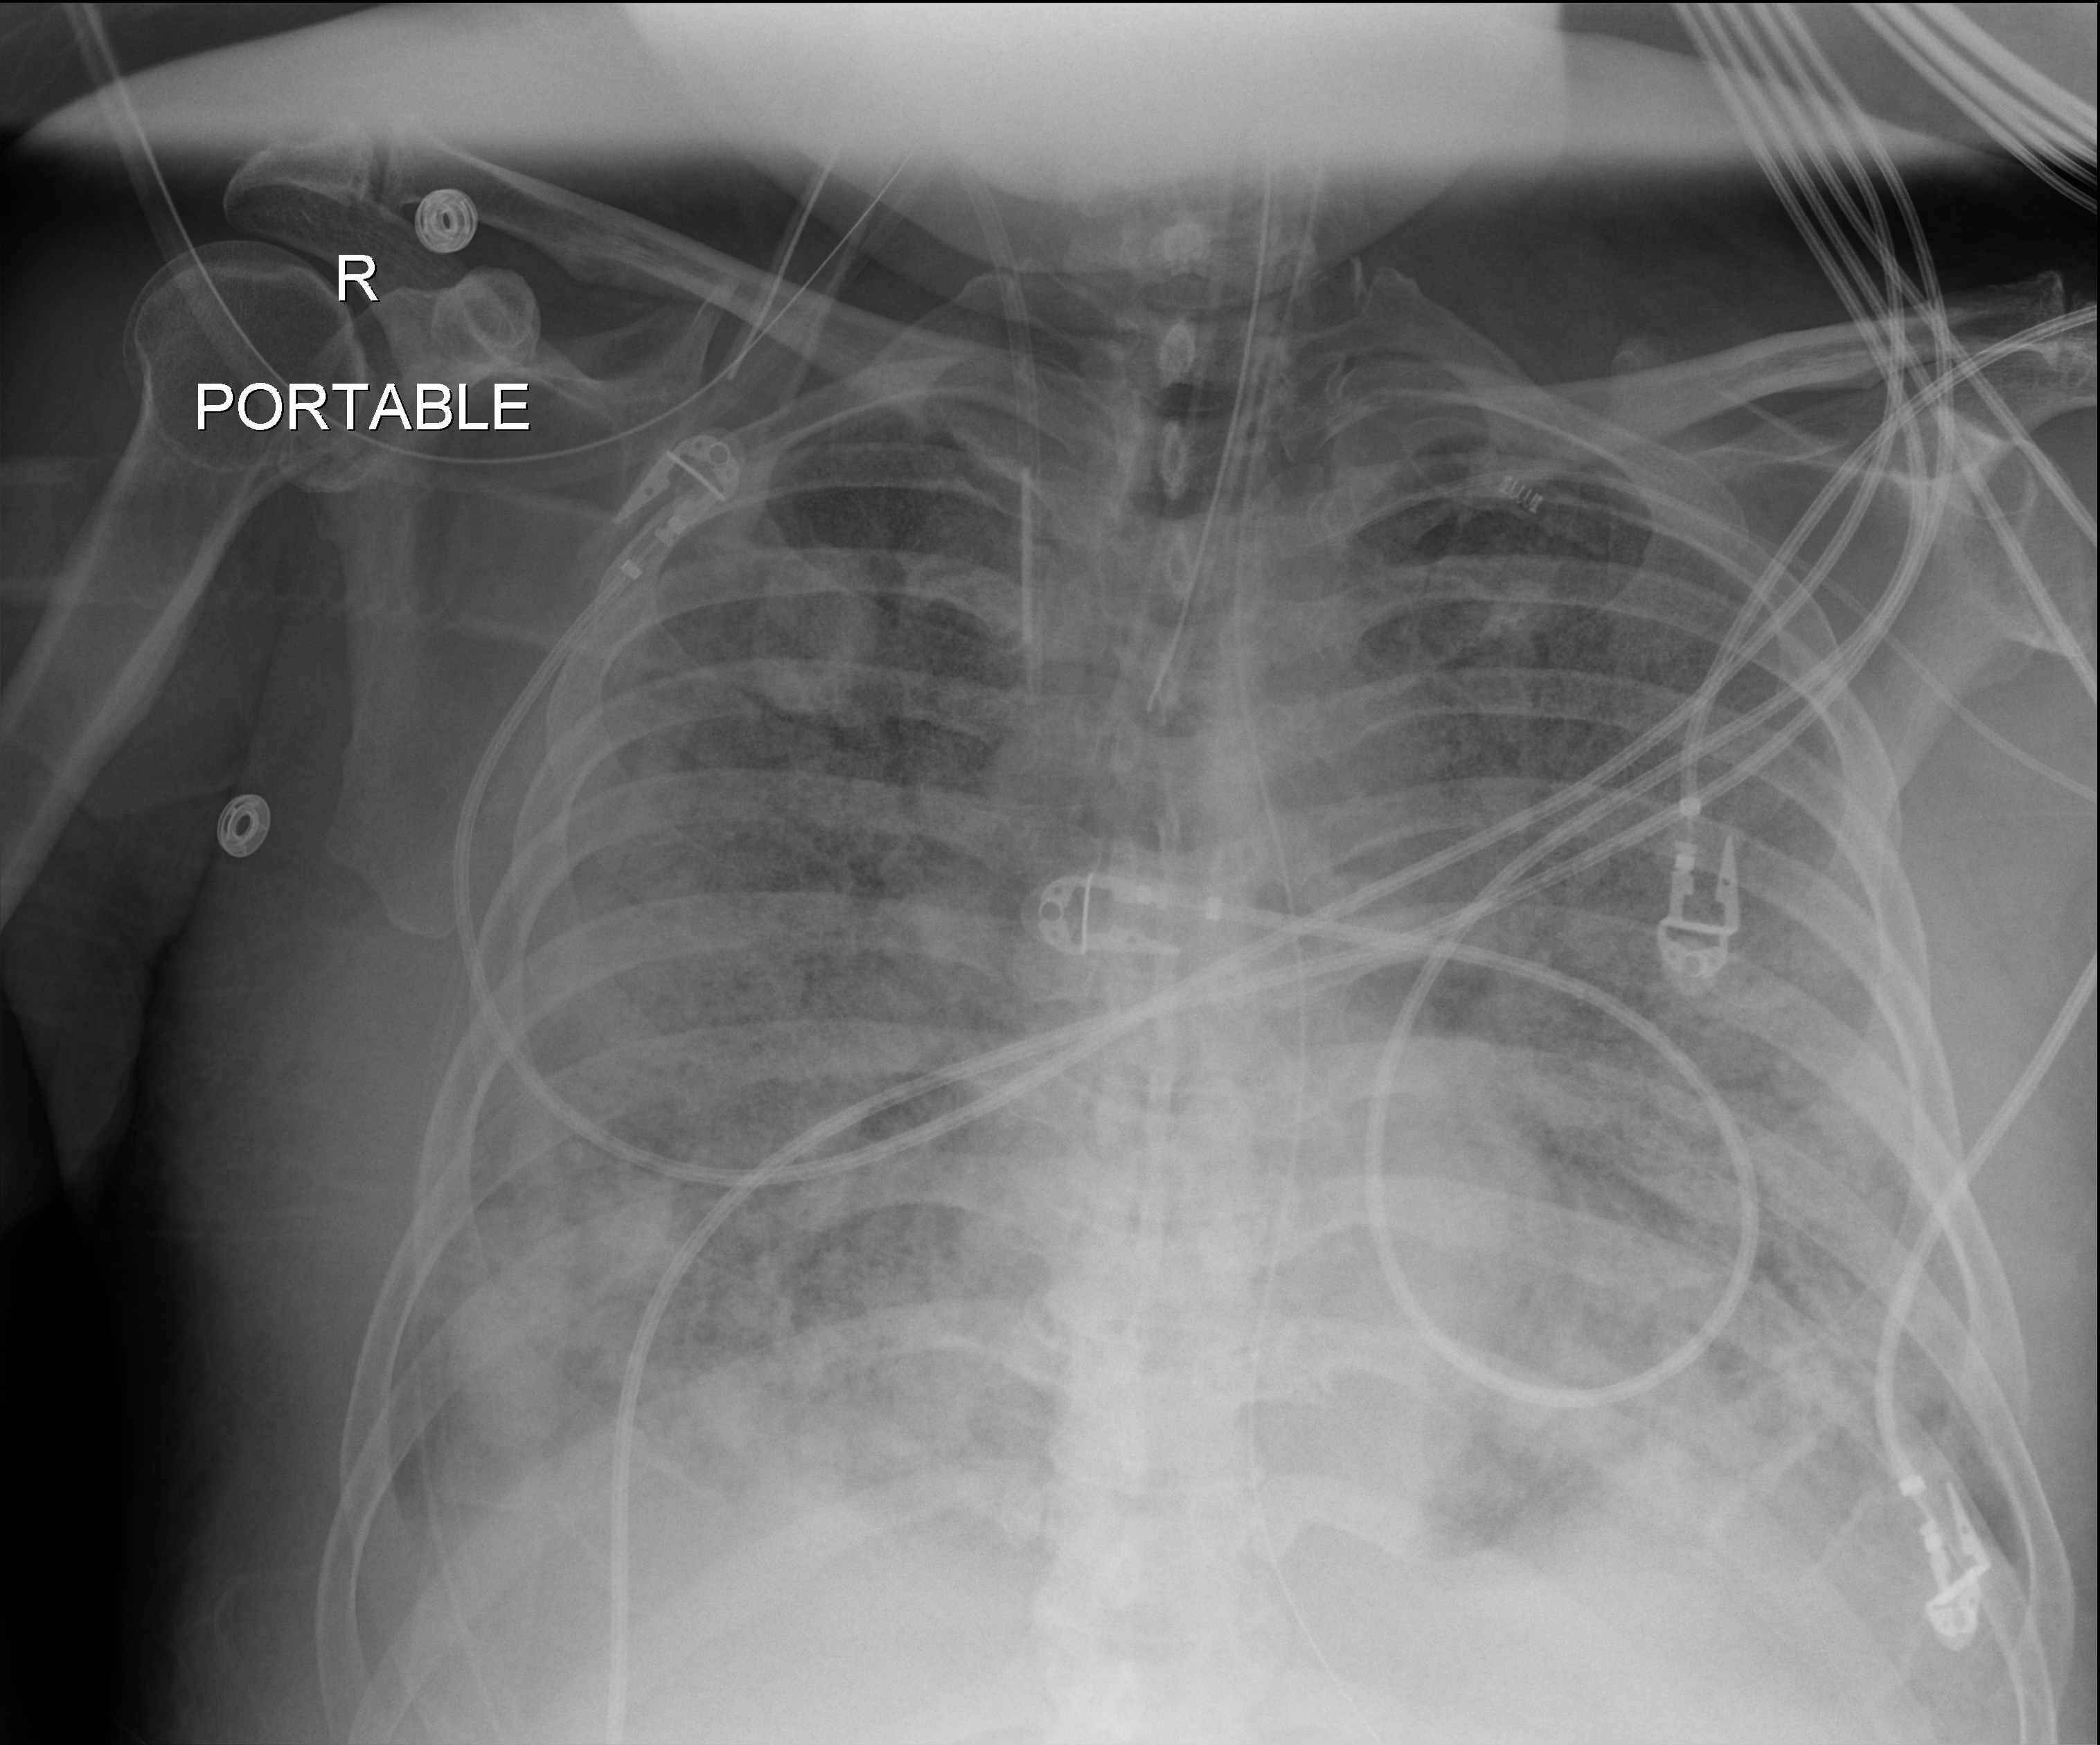
Bedside chest radiograph (digital radiography), anteroposterior (AP) projection. Patient hospitalised with COVID-19; male, aged 60–74 years.
From the hospital-stay record, not from the radiograph (when in the stay this image was taken is not recorded): chronic kidney disease (admission record): no; COPD (admission record): no; admitted to intensive care during this hospital stay: yes.